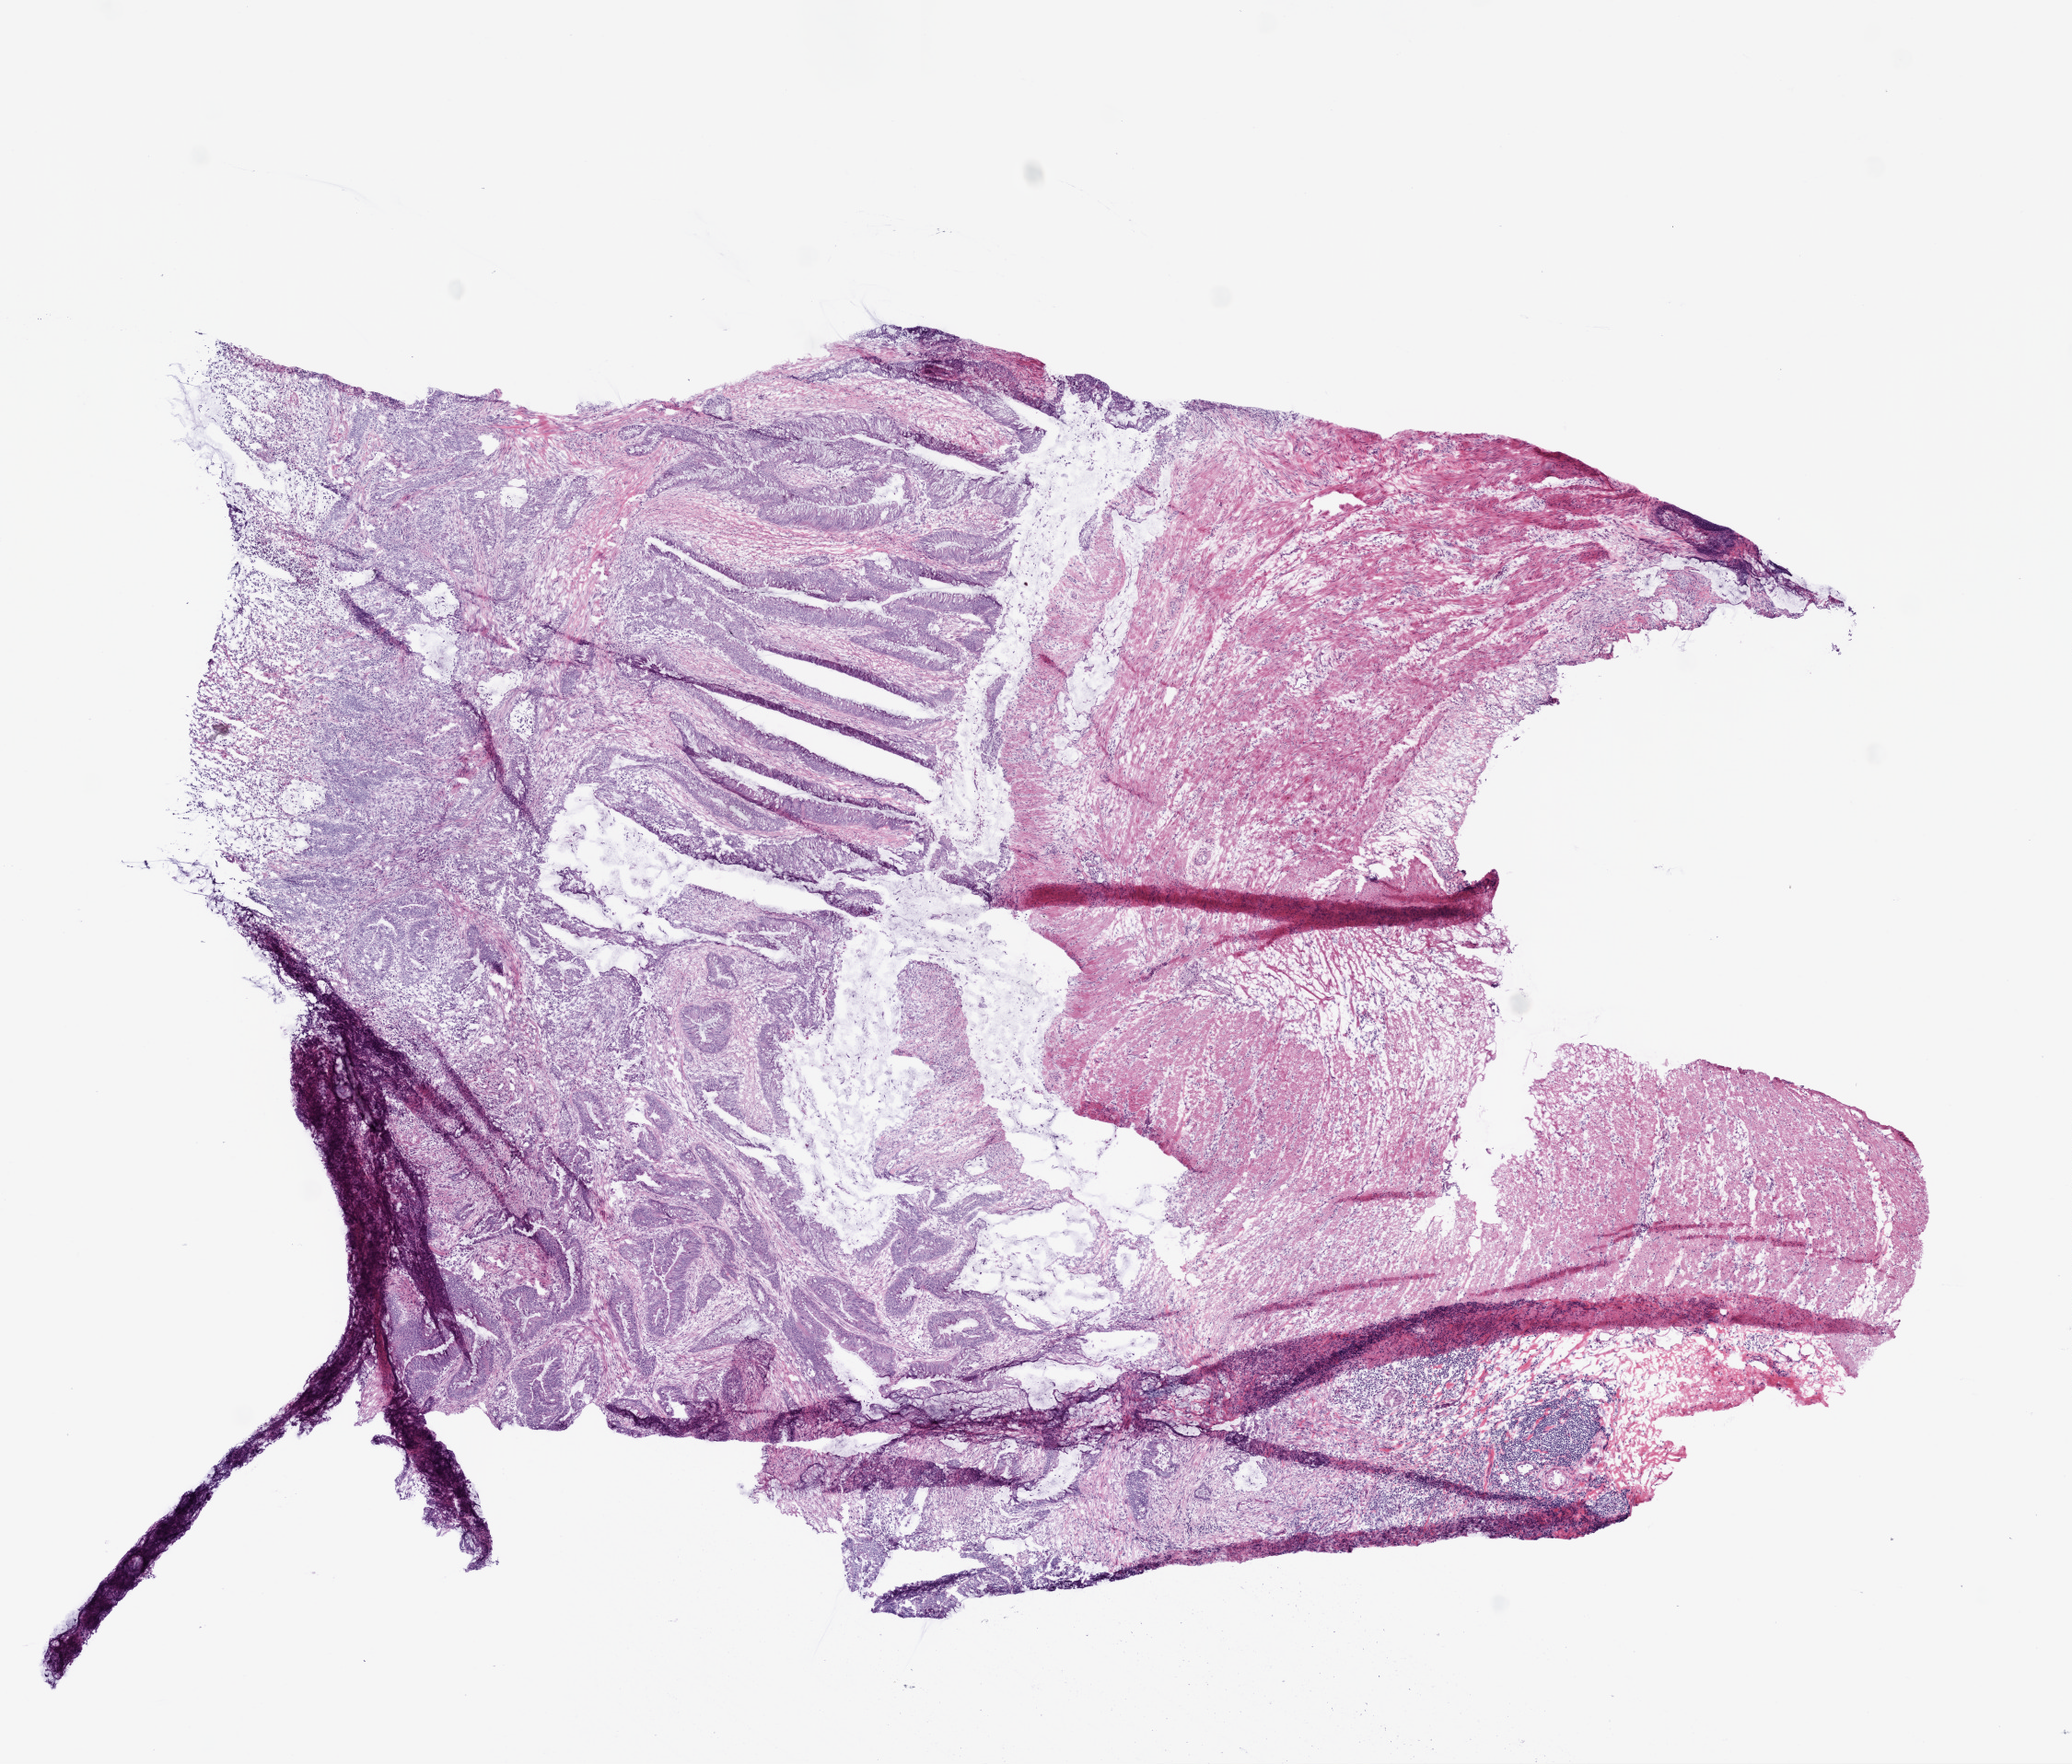
Whole-slide histology image, Hematoxylin and eosin (H&E) stained — a low-resolution overview of the entire scanned area, about 9.0 x 7.7 mm, frozen section from the bottom of the tissue portion, rectum, primary tumour sample. Female, age 67 years at initial diagnosis. Pathologist review of this section (percent, as recorded): tumour cells 30%, tumour nuclei 65%, normal cells 40%, stromal cells 15%, necrosis 15%.
Diagnosis: Mucinous adenocarcinoma (rectosigmoid junction). TNM: T3 N1 M0. AJCC pathologic stage: IIIB (6th edition).